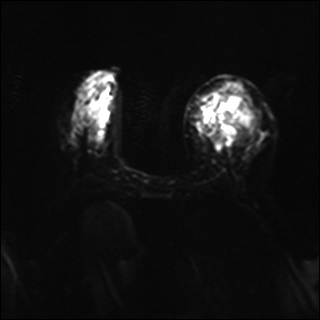
Breast MRI, one axial slice; position 13 of 37 along the scan axis; diffusion-weighted series; image 2 of 4 stored at this slice position (different b-values; order by instance number); 1.5 T; 320 × 320 image matrix. Female patient.
Outlined on this slice (manually delineated by an expert):
- tumour on diffusion-weighted imaging: bounding box [x1, y1, x2, y2] px = [218, 92, 251, 135]